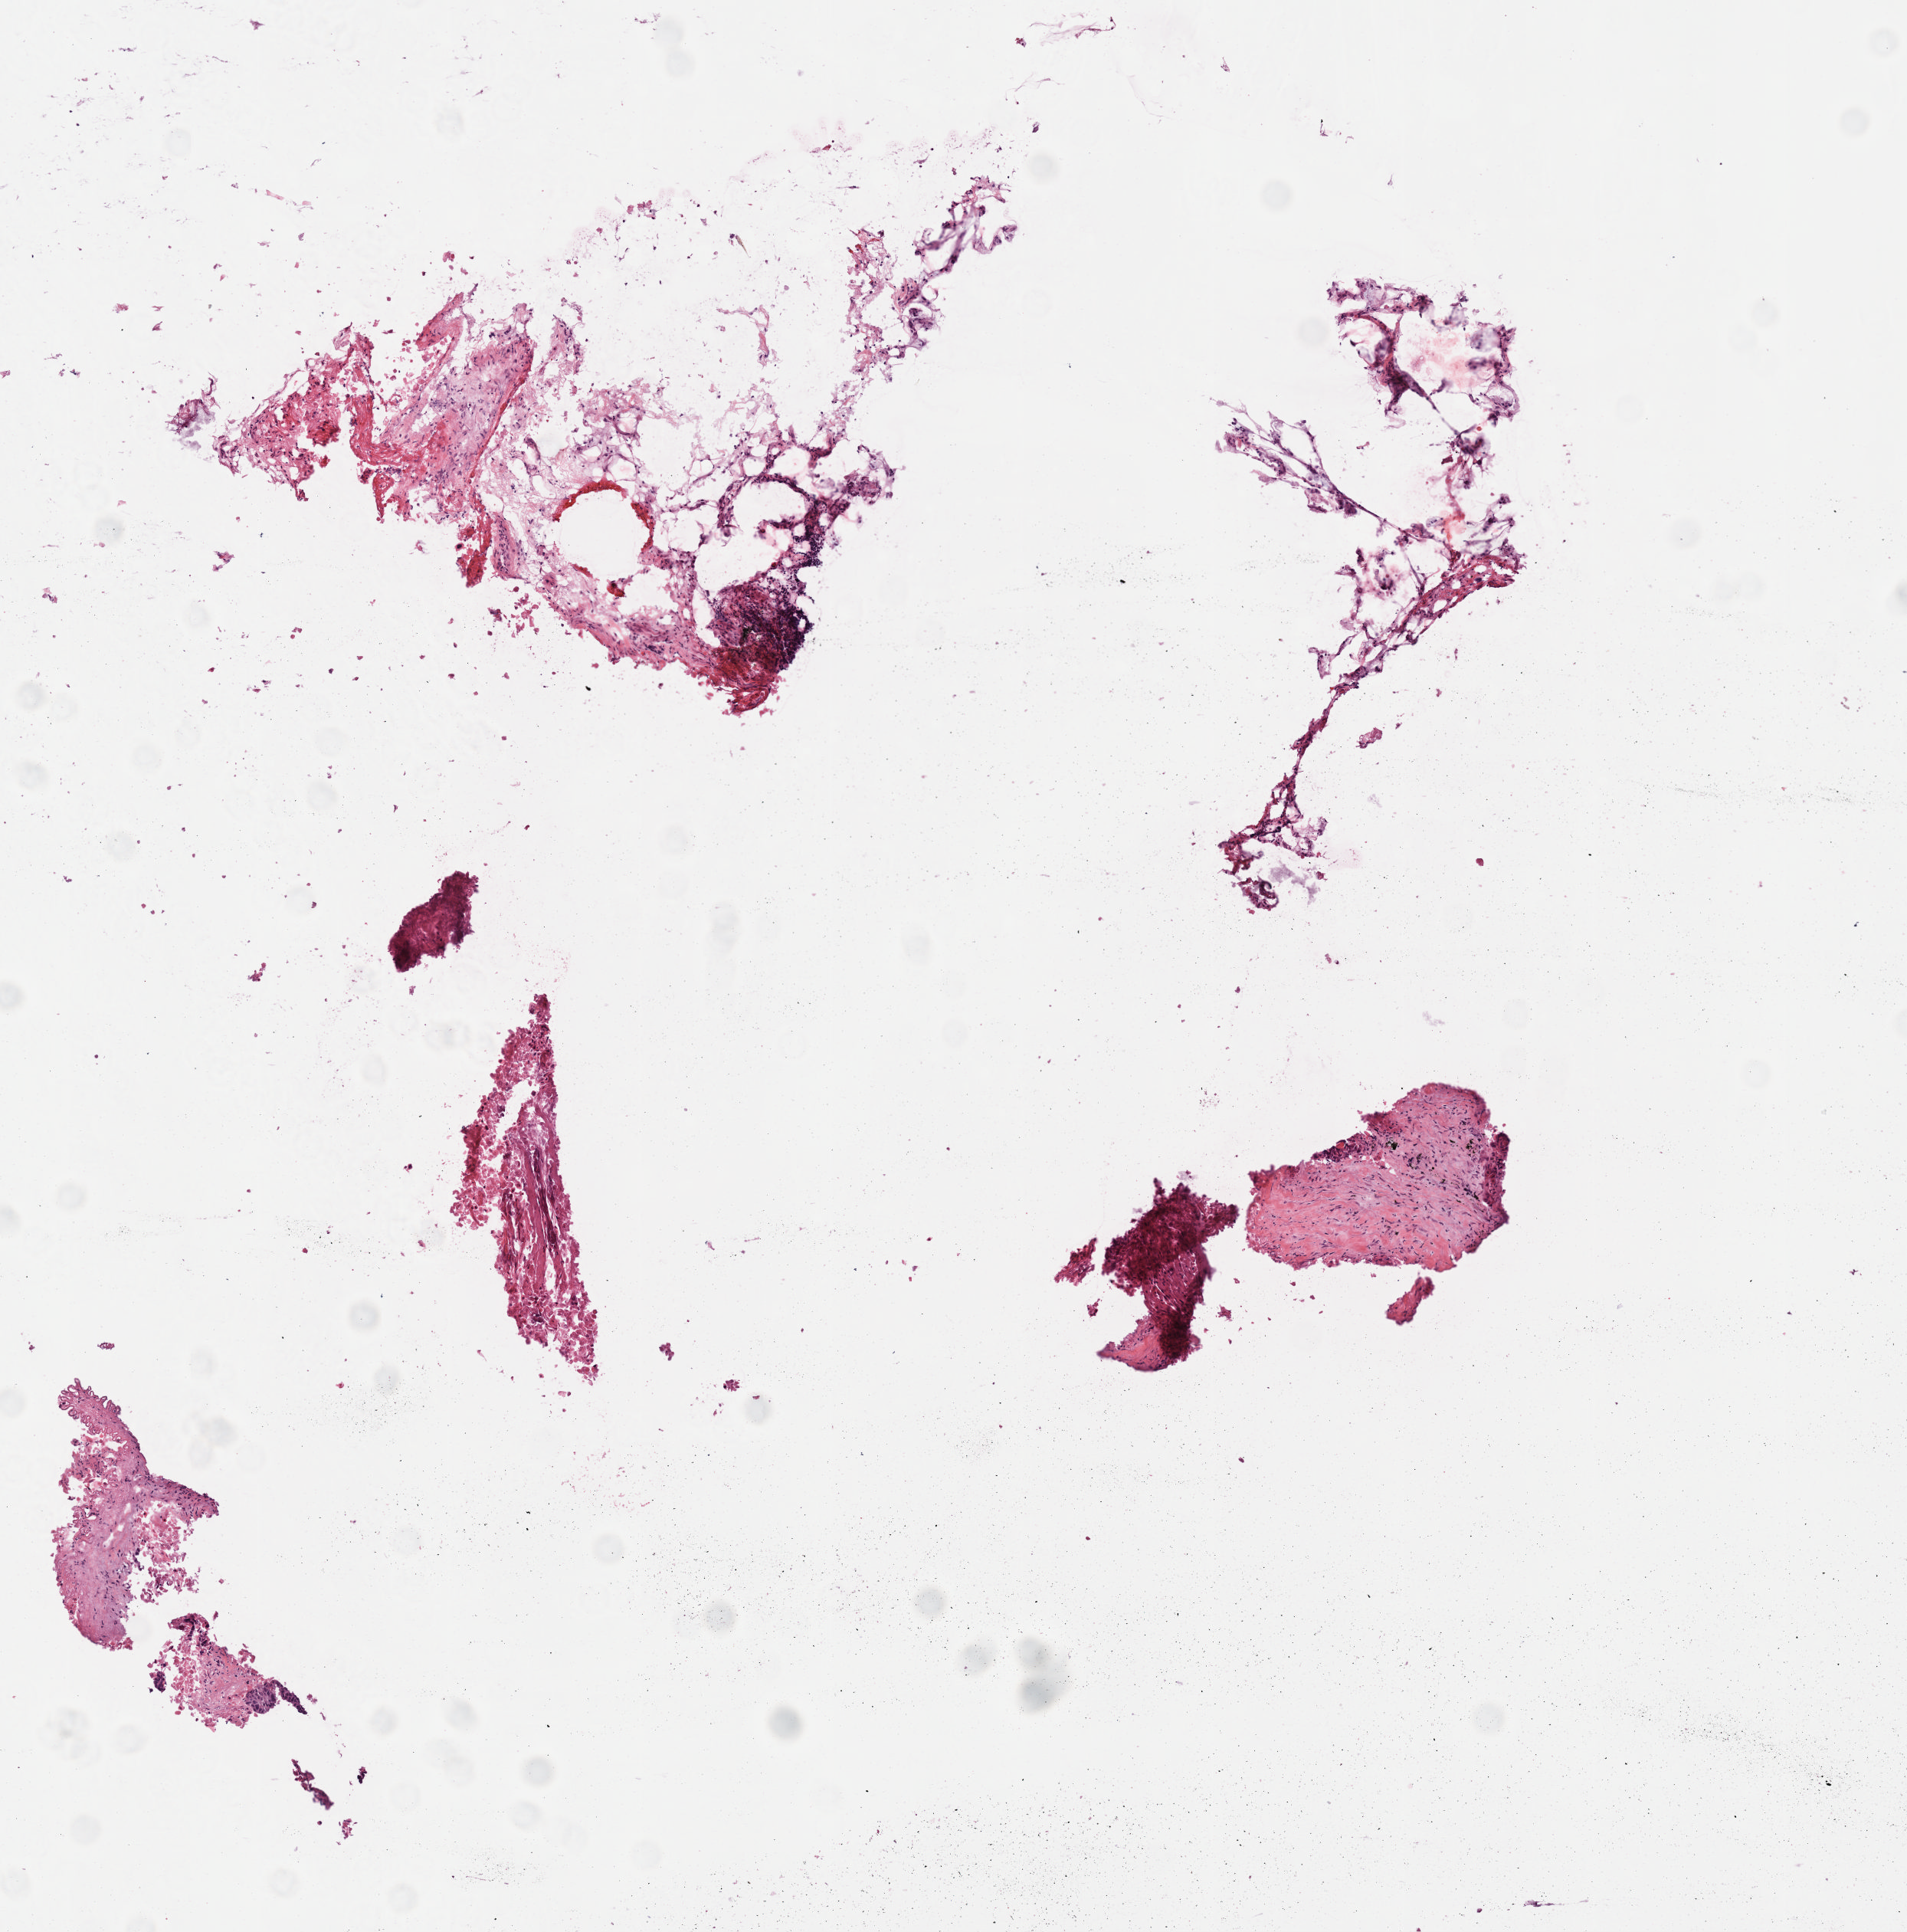
Whole-slide histology image, Hematoxylin and eosin (H&E) stained — low-resolution overview of the scanned area, about 5.0 x 5.1 mm; frozen section; lung, primary tumour sample. Male patient. Slide review estimates, as recorded: tumour cells 58%, tumour nuclei 70%, normal cells 0%, stromal cells 30%, necrosis 12%. Infiltration values recorded for this section: lymphocyte infiltration 10%.
TNM: T3 N1 M0. Diagnosis: Squamous cell carcinoma, NOS. Laterality: left. AJCC pathologic stage: IIIA.